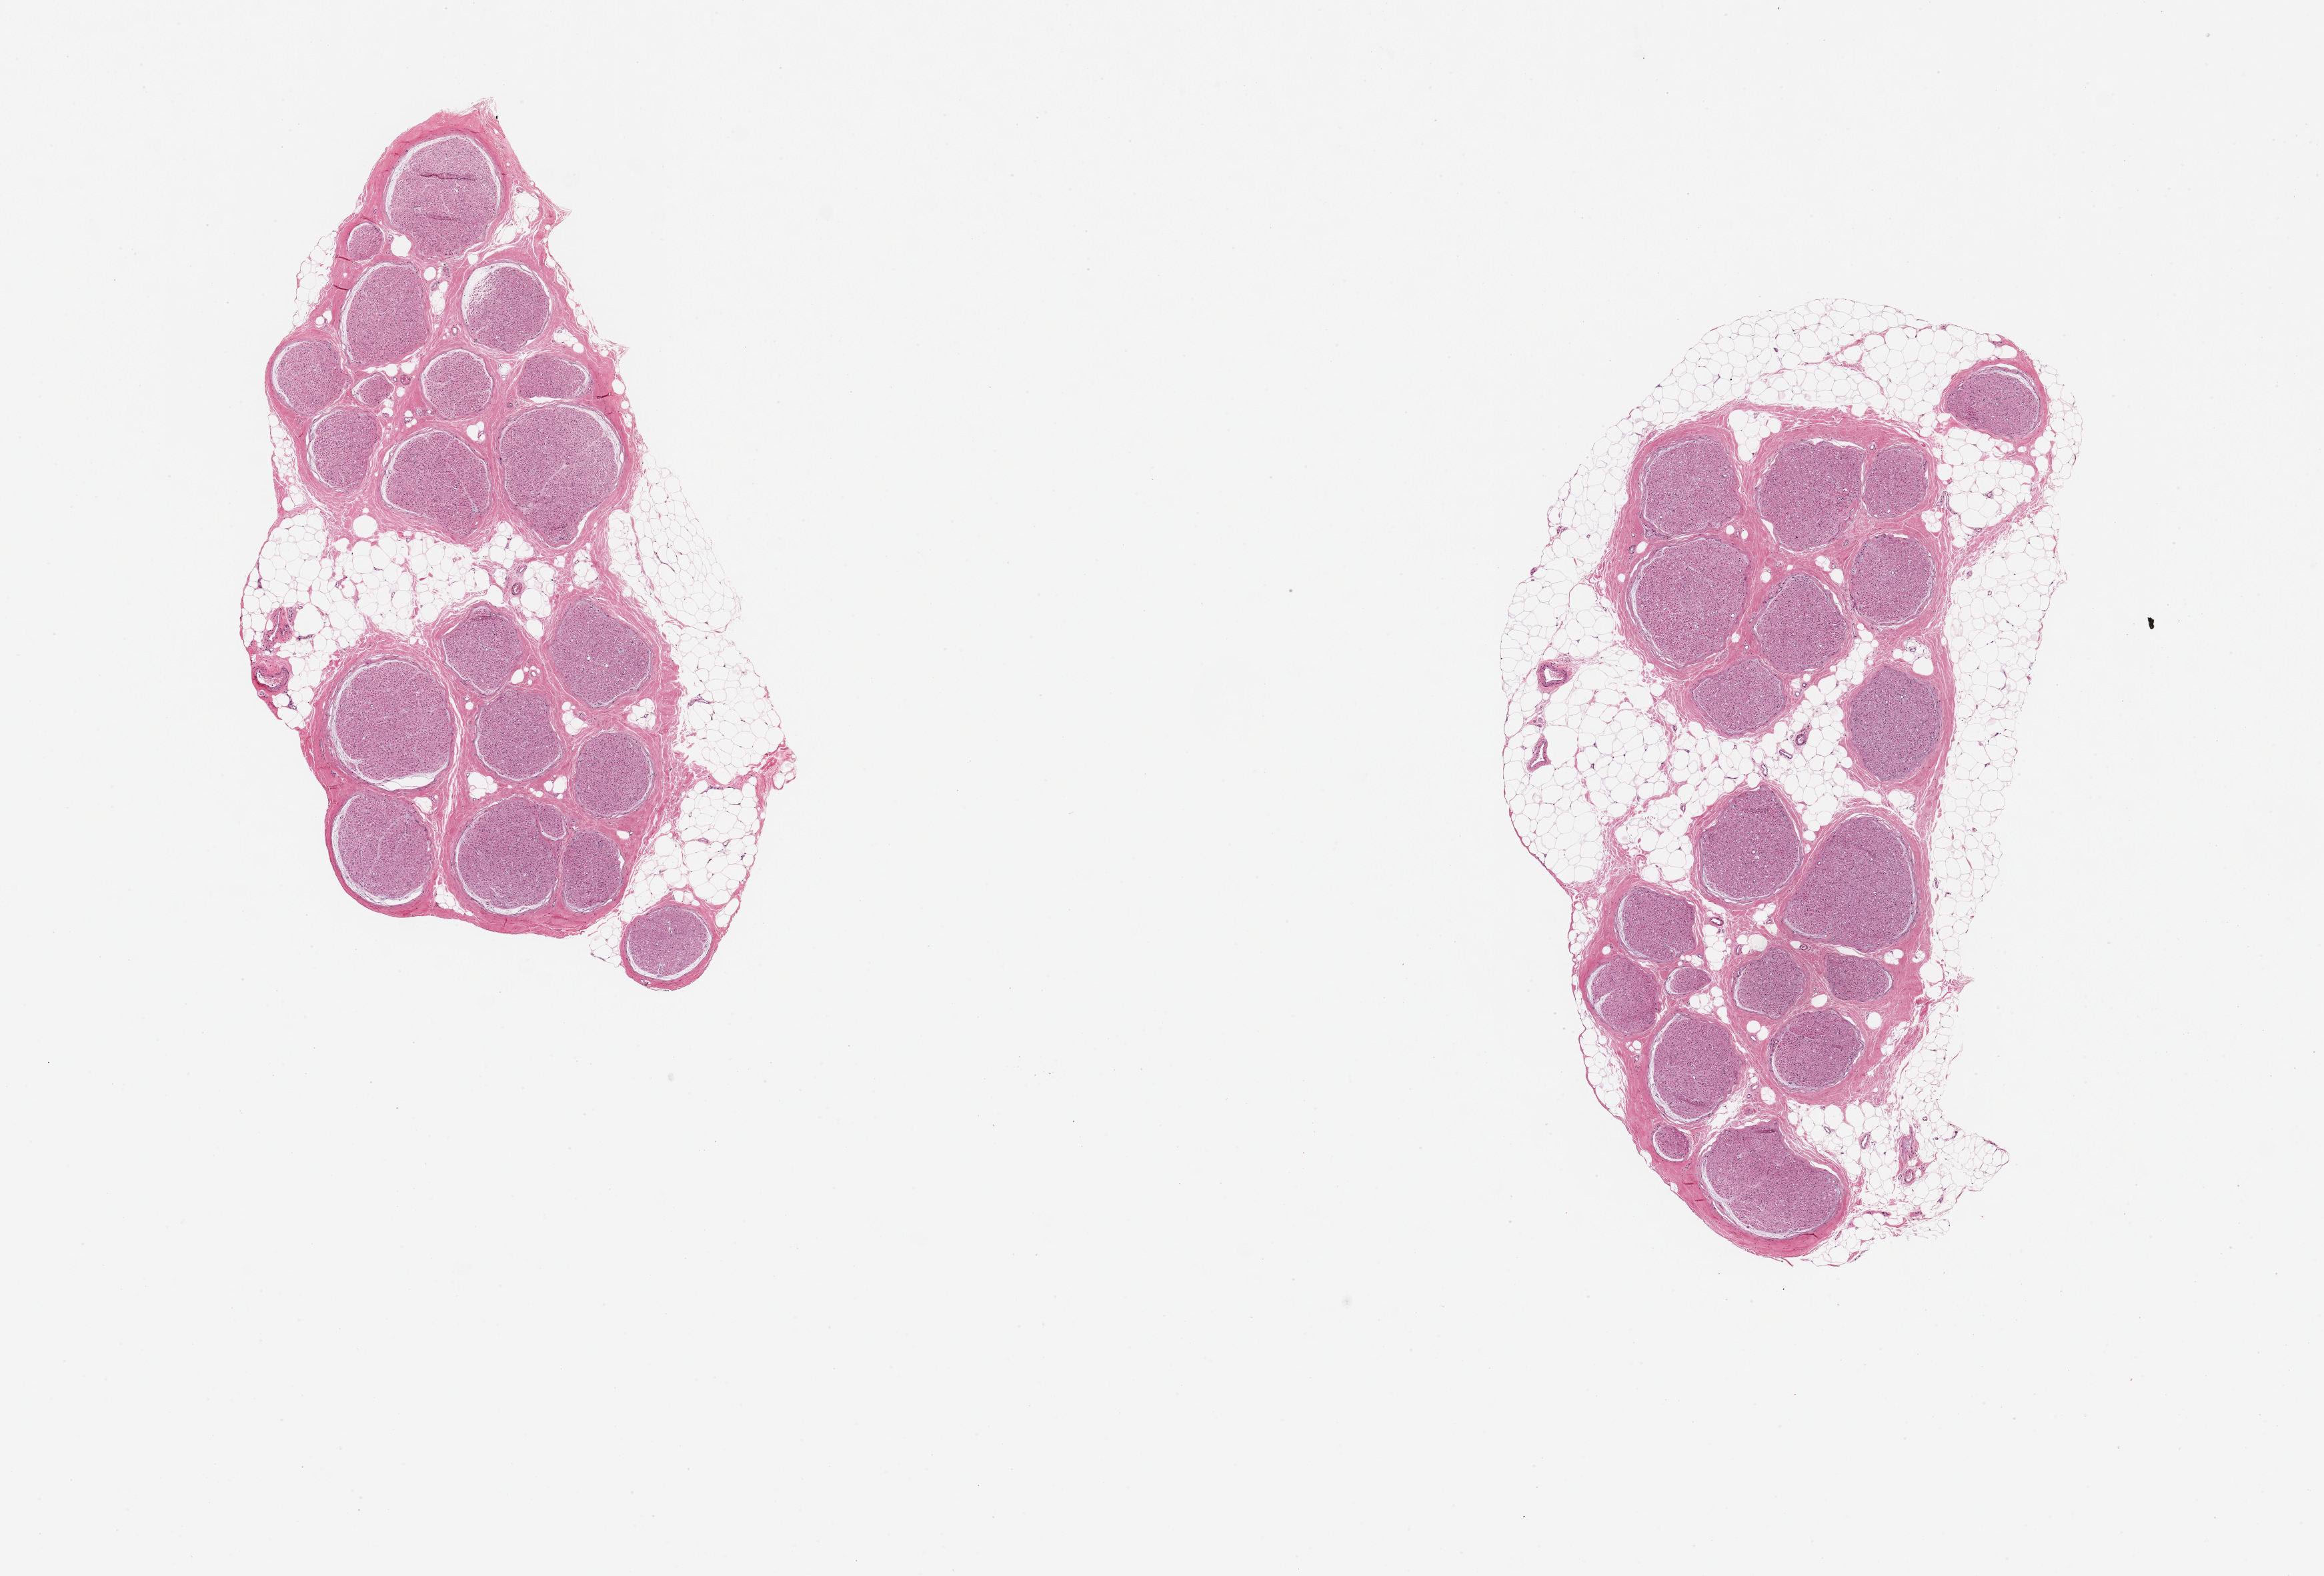
Whole-slide image, hematoxylin and eosin (H&E) stain — a low-resolution overview of the entire scanned area, about 13.8 x 9.3 mm; PAXgene-fixed paraffin-embedded (PFPE) section; sampled site (target tissue): tibial nerve; tissue donor sample. Donor sex: female.
Reviewer comment on this tissue sample: 2 pieces, 5x3 & 6x3mm; ~.5mm adherent discontinuous fat.